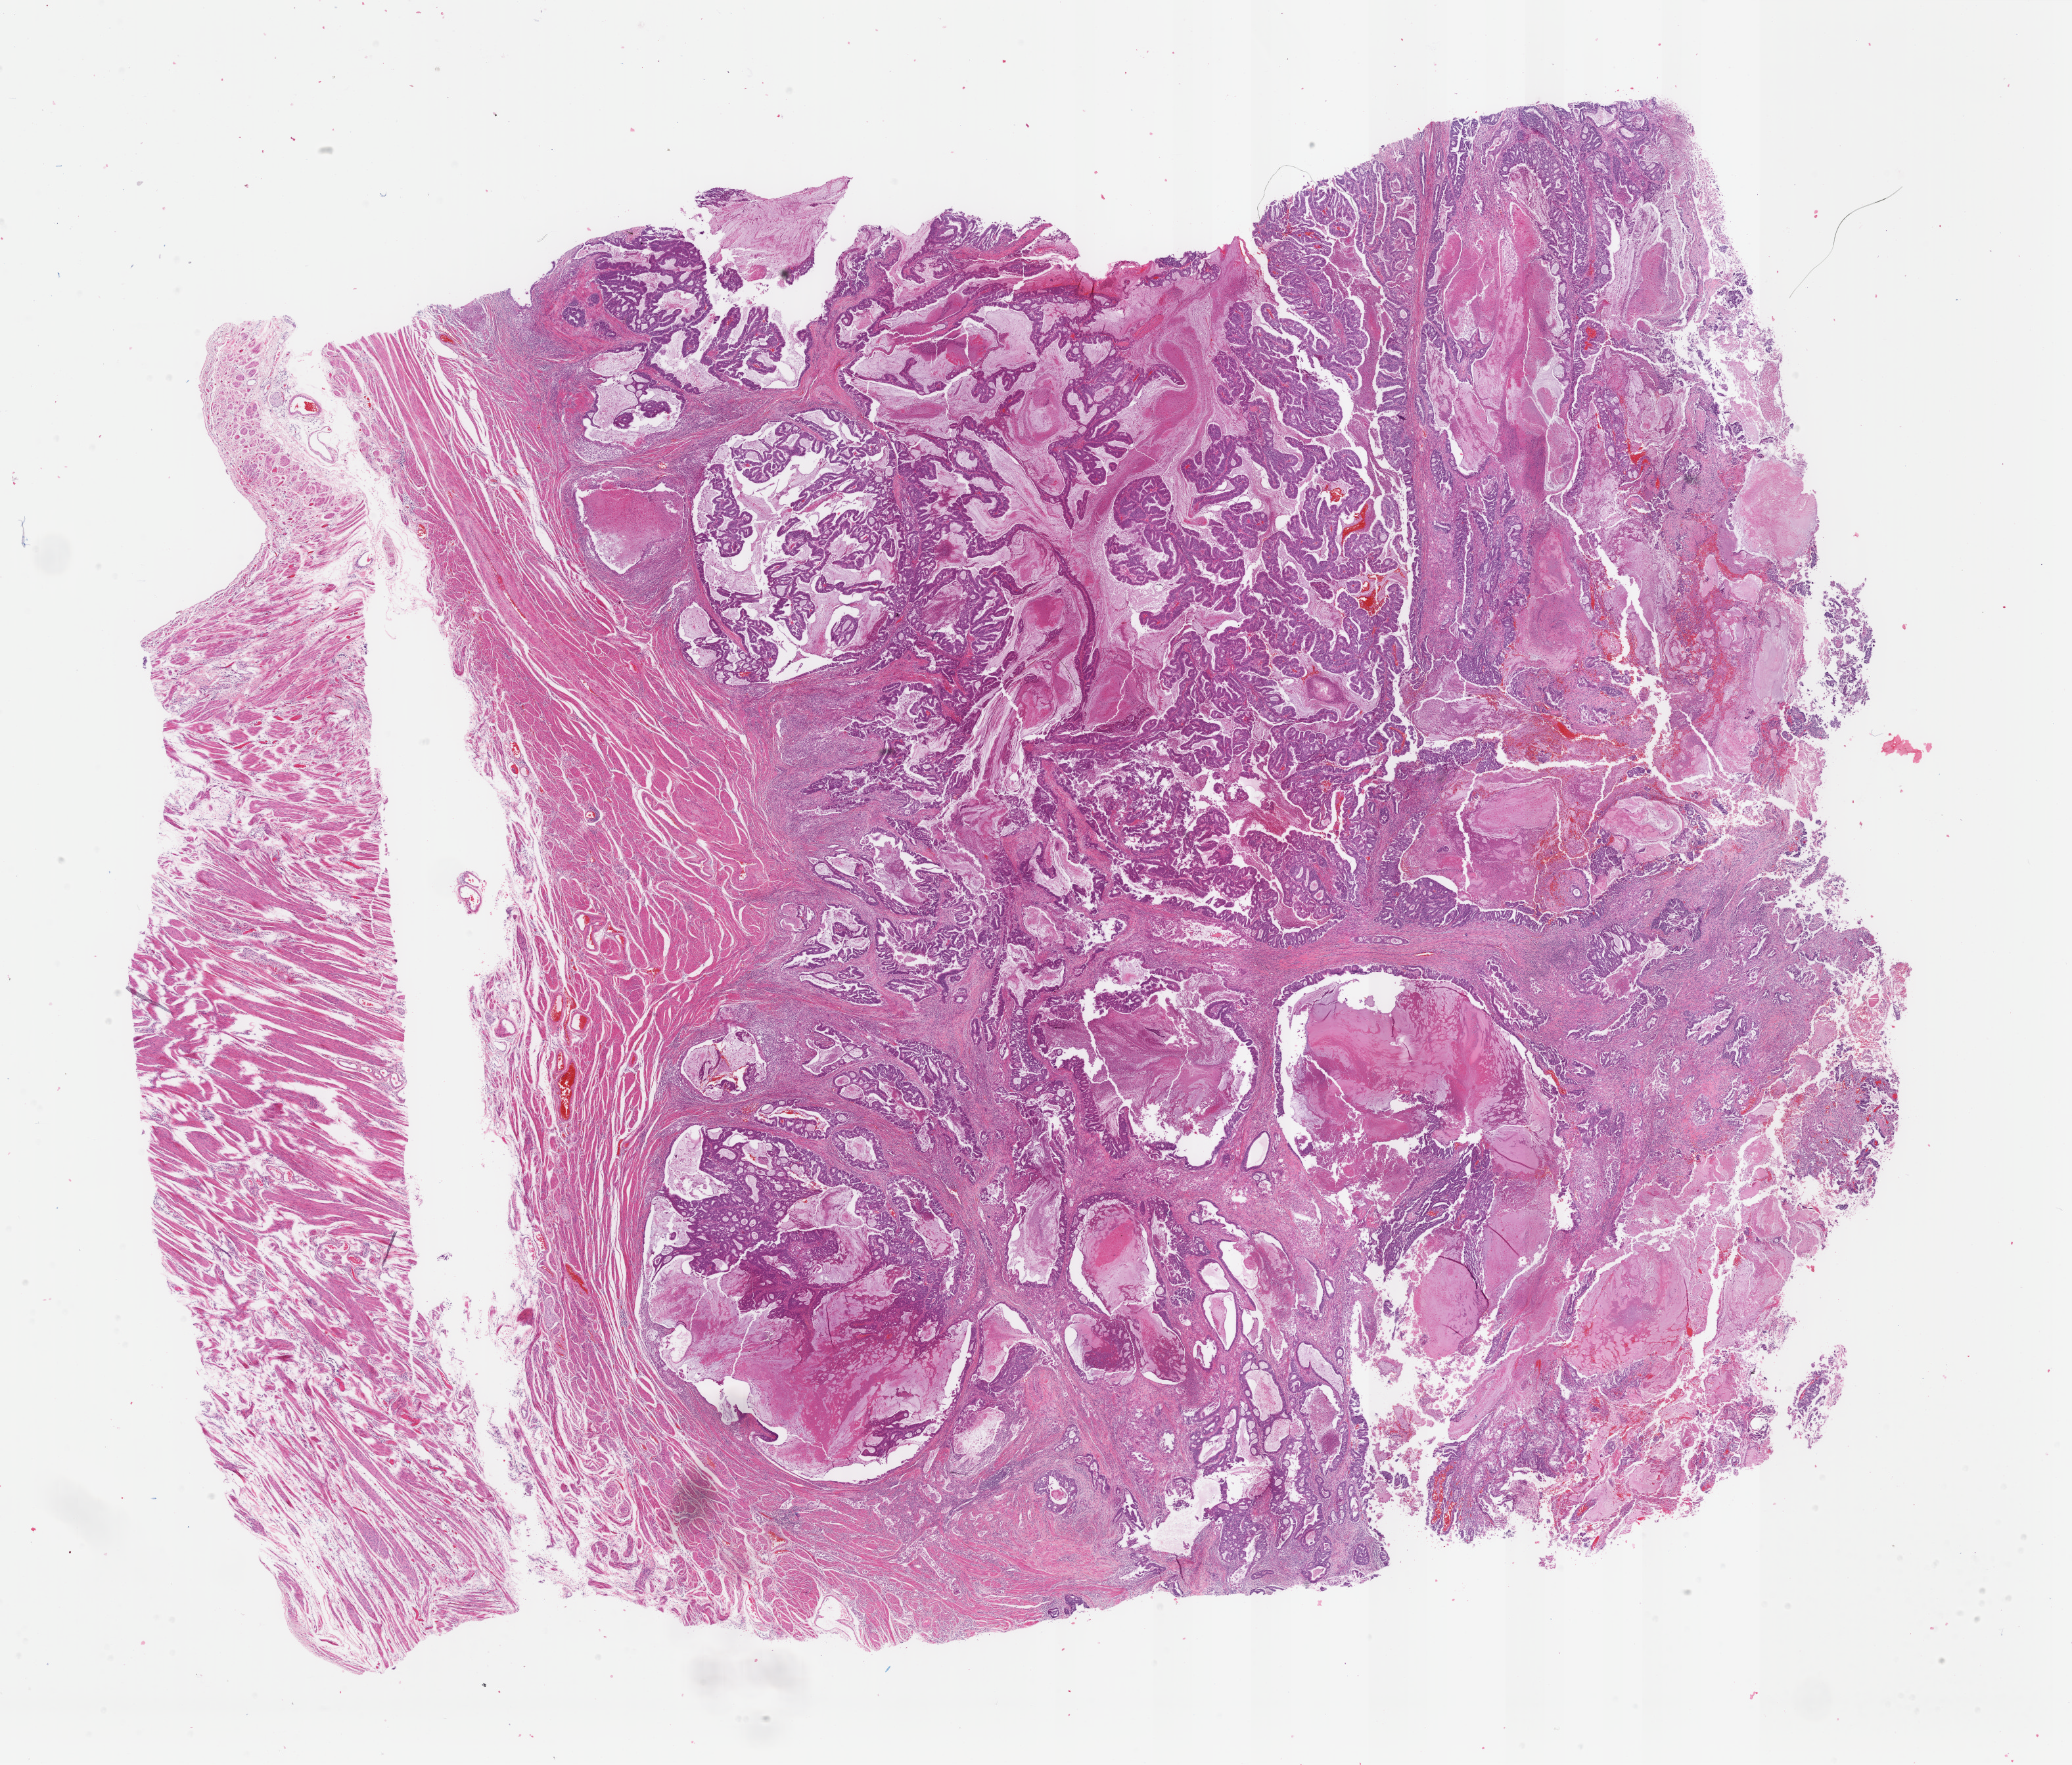
H&E whole-slide image — shown as a low-resolution overview of the whole scanned area (about 25.0 x 21.3 mm, acquisition: 40x scan). Formalin-fixed paraffin-embedded (FFPE) diagnostic section. Uterus, primary tumour sample. Patient: female, age at initial diagnosis 88 years.
Histologic diagnosis: Endometrioid adenocarcinoma, NOS.